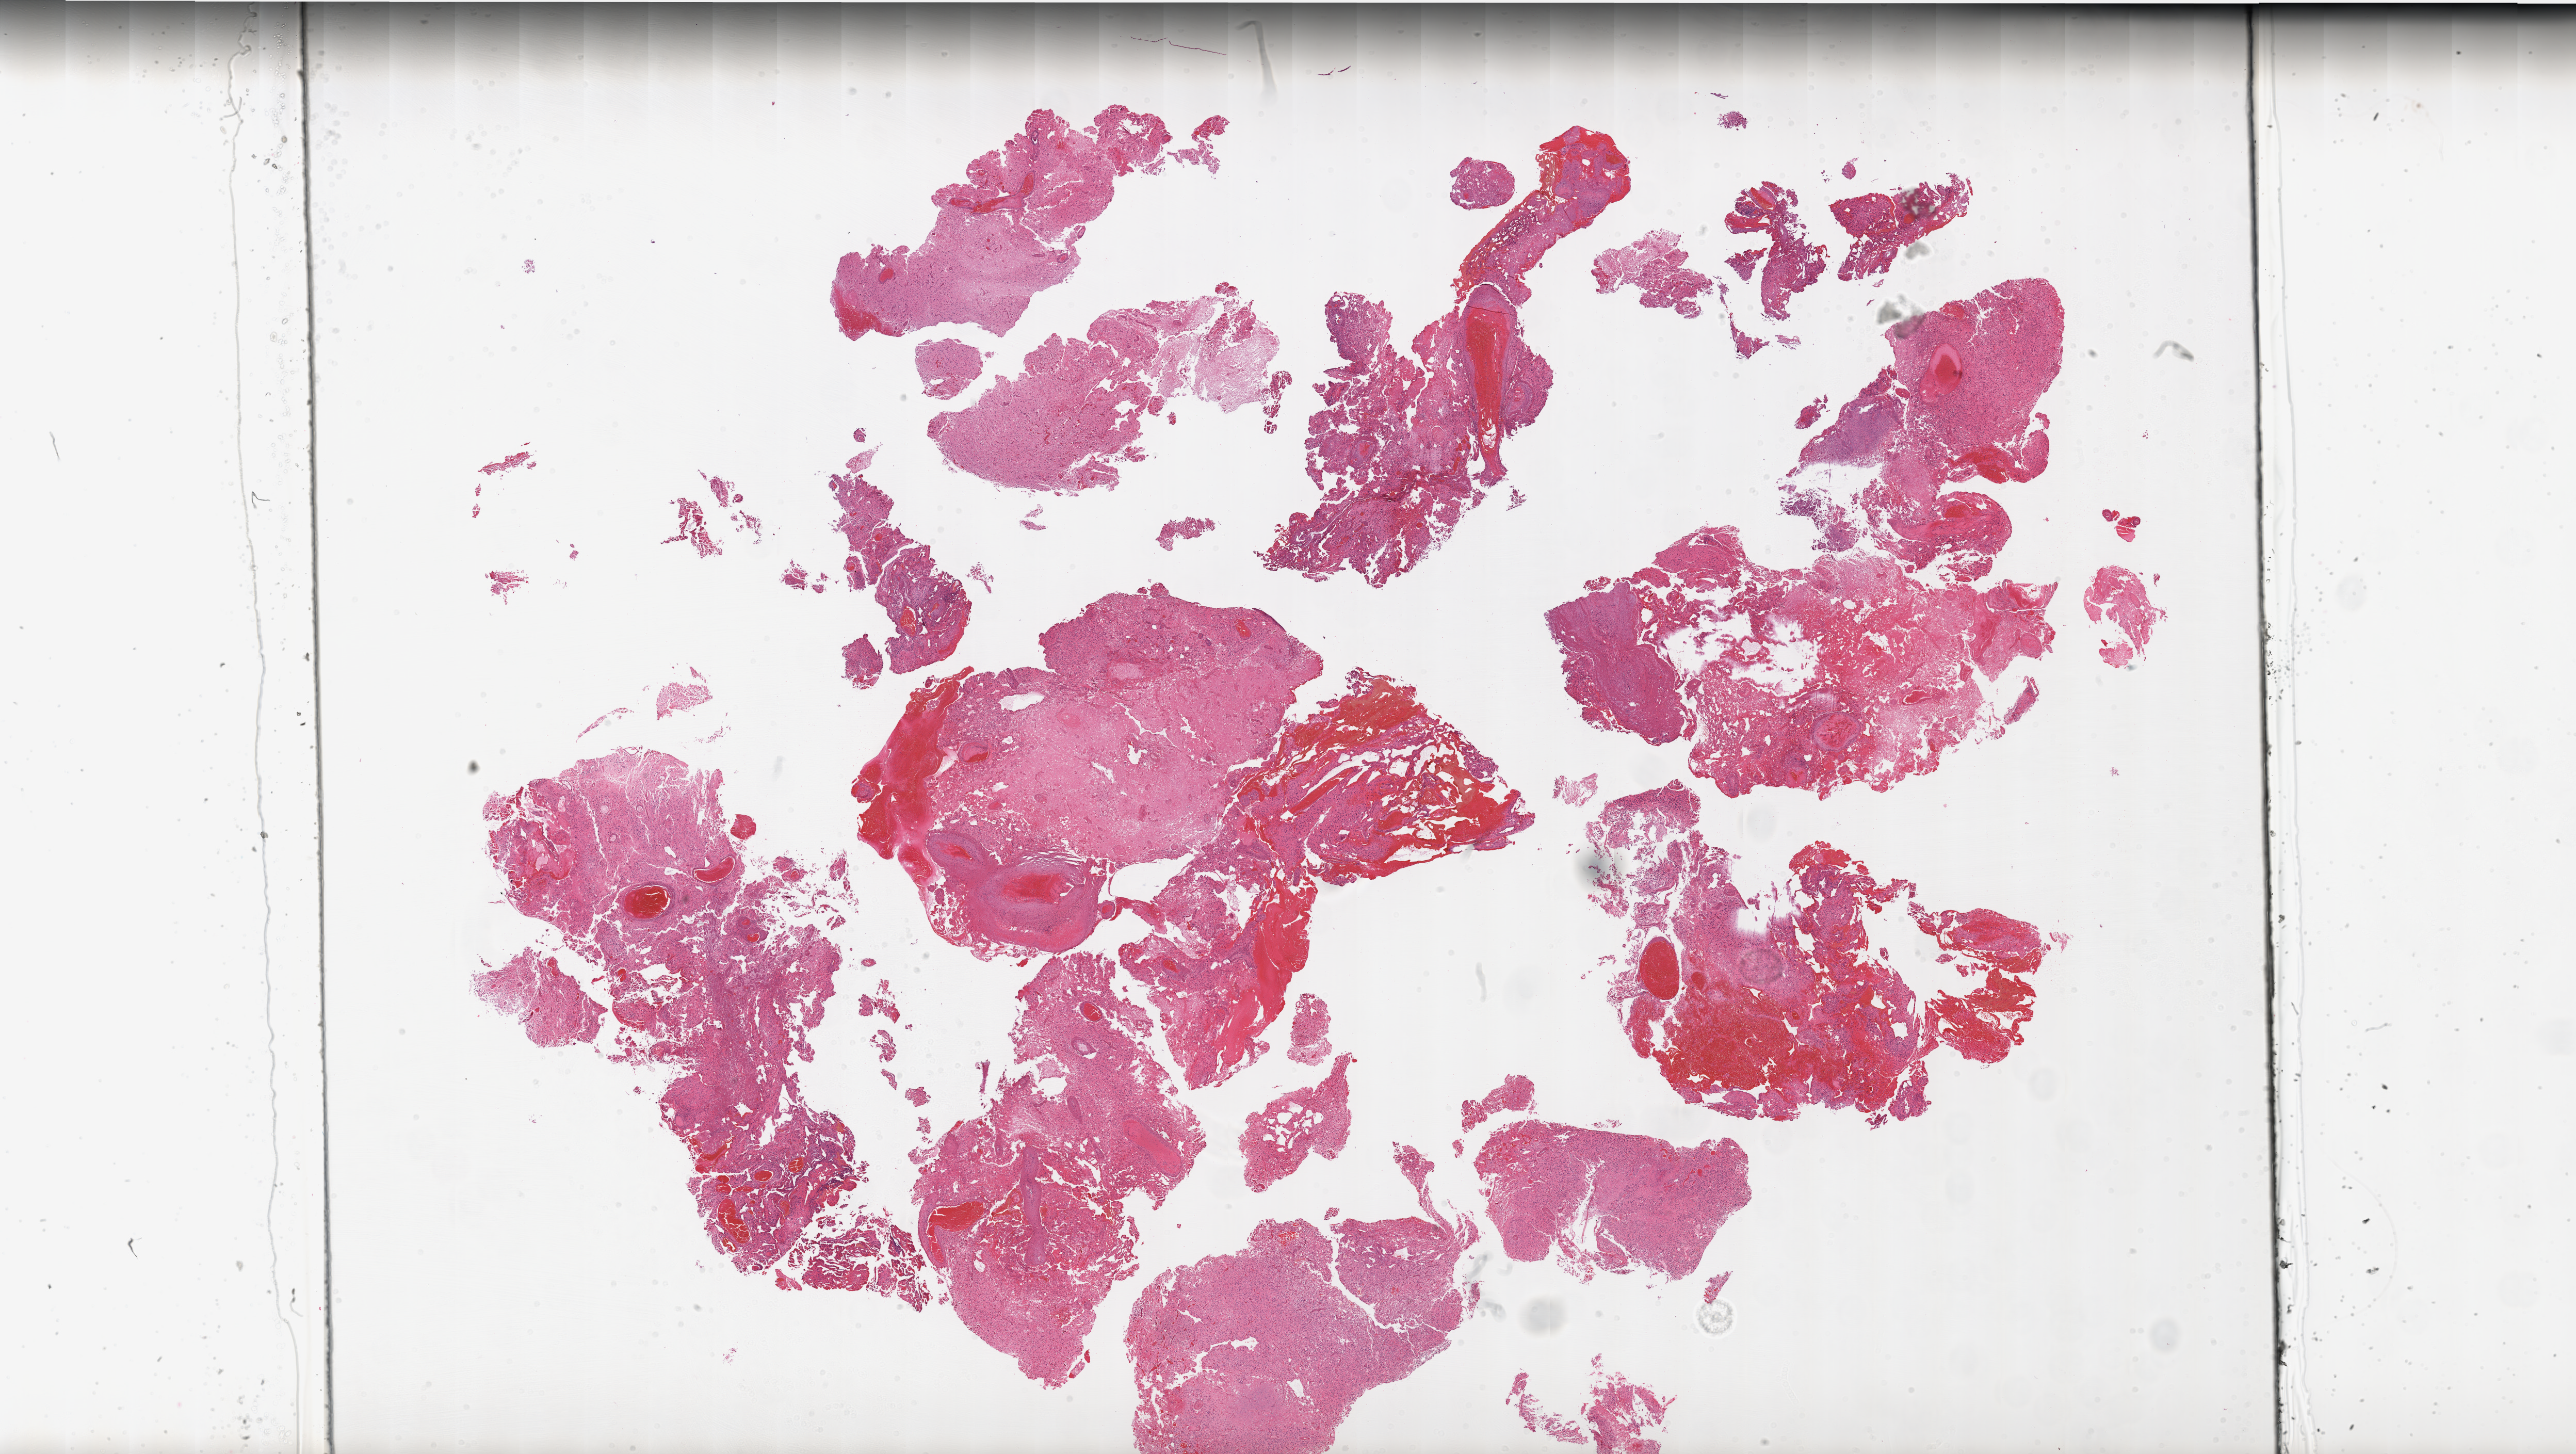
Whole-slide histology image, Hematoxylin and eosin (H&E) stained, low-resolution overview of the scanned area, about 40.0 x 22.6 mm (acquisition: 20x scan); FFPE section; sample: primary tumour, brain. Male patient; age at initial diagnosis 76 years.
Pathologic diagnosis: Glioblastoma.